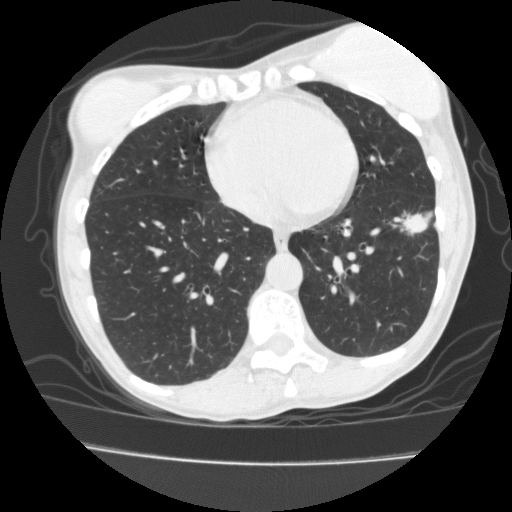
Low-dose screening chest CT, one axial slice; position 62 of 171 along the scan axis; reconstruction kernel FC10; lung window (W 1500 / L -600 HU); 2 mm slice thickness; 512 × 512 image matrix, field of view 339 × 339 mm.
Structures marked on this image (expert manual segmentation):
- lesion 1 (tumor, lower lobe of left lung): bounding box <405,215,427,234> (left, top, right, bottom; pixels)